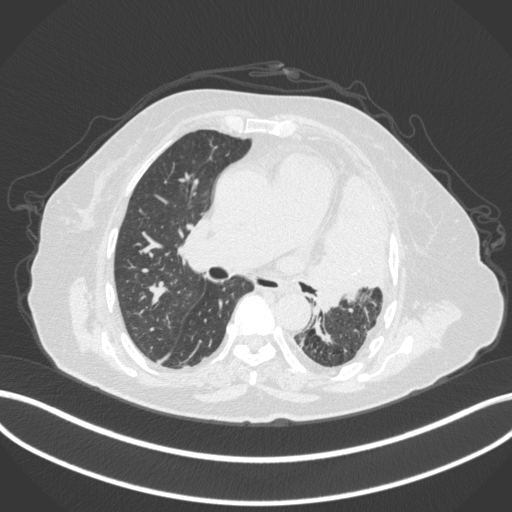
Chest CT, one axial slice. Position 214 of 399 along the scan axis. Reconstruction kernel B31f. Lung window (W 1500 / L -600 HU). 512 × 512 image matrix. Female patient, age 75 years. Case-level facts recorded for this patient, not image findings: clinical TNM (as recorded): T3 N3 M1.
Outlined on this slice (bounding box drawn by a radiologist):
- lung tumour (recorded histology: adenocarcinoma): bounding box (x1, y1, x2, y2) in pixels: (298, 169, 389, 313)